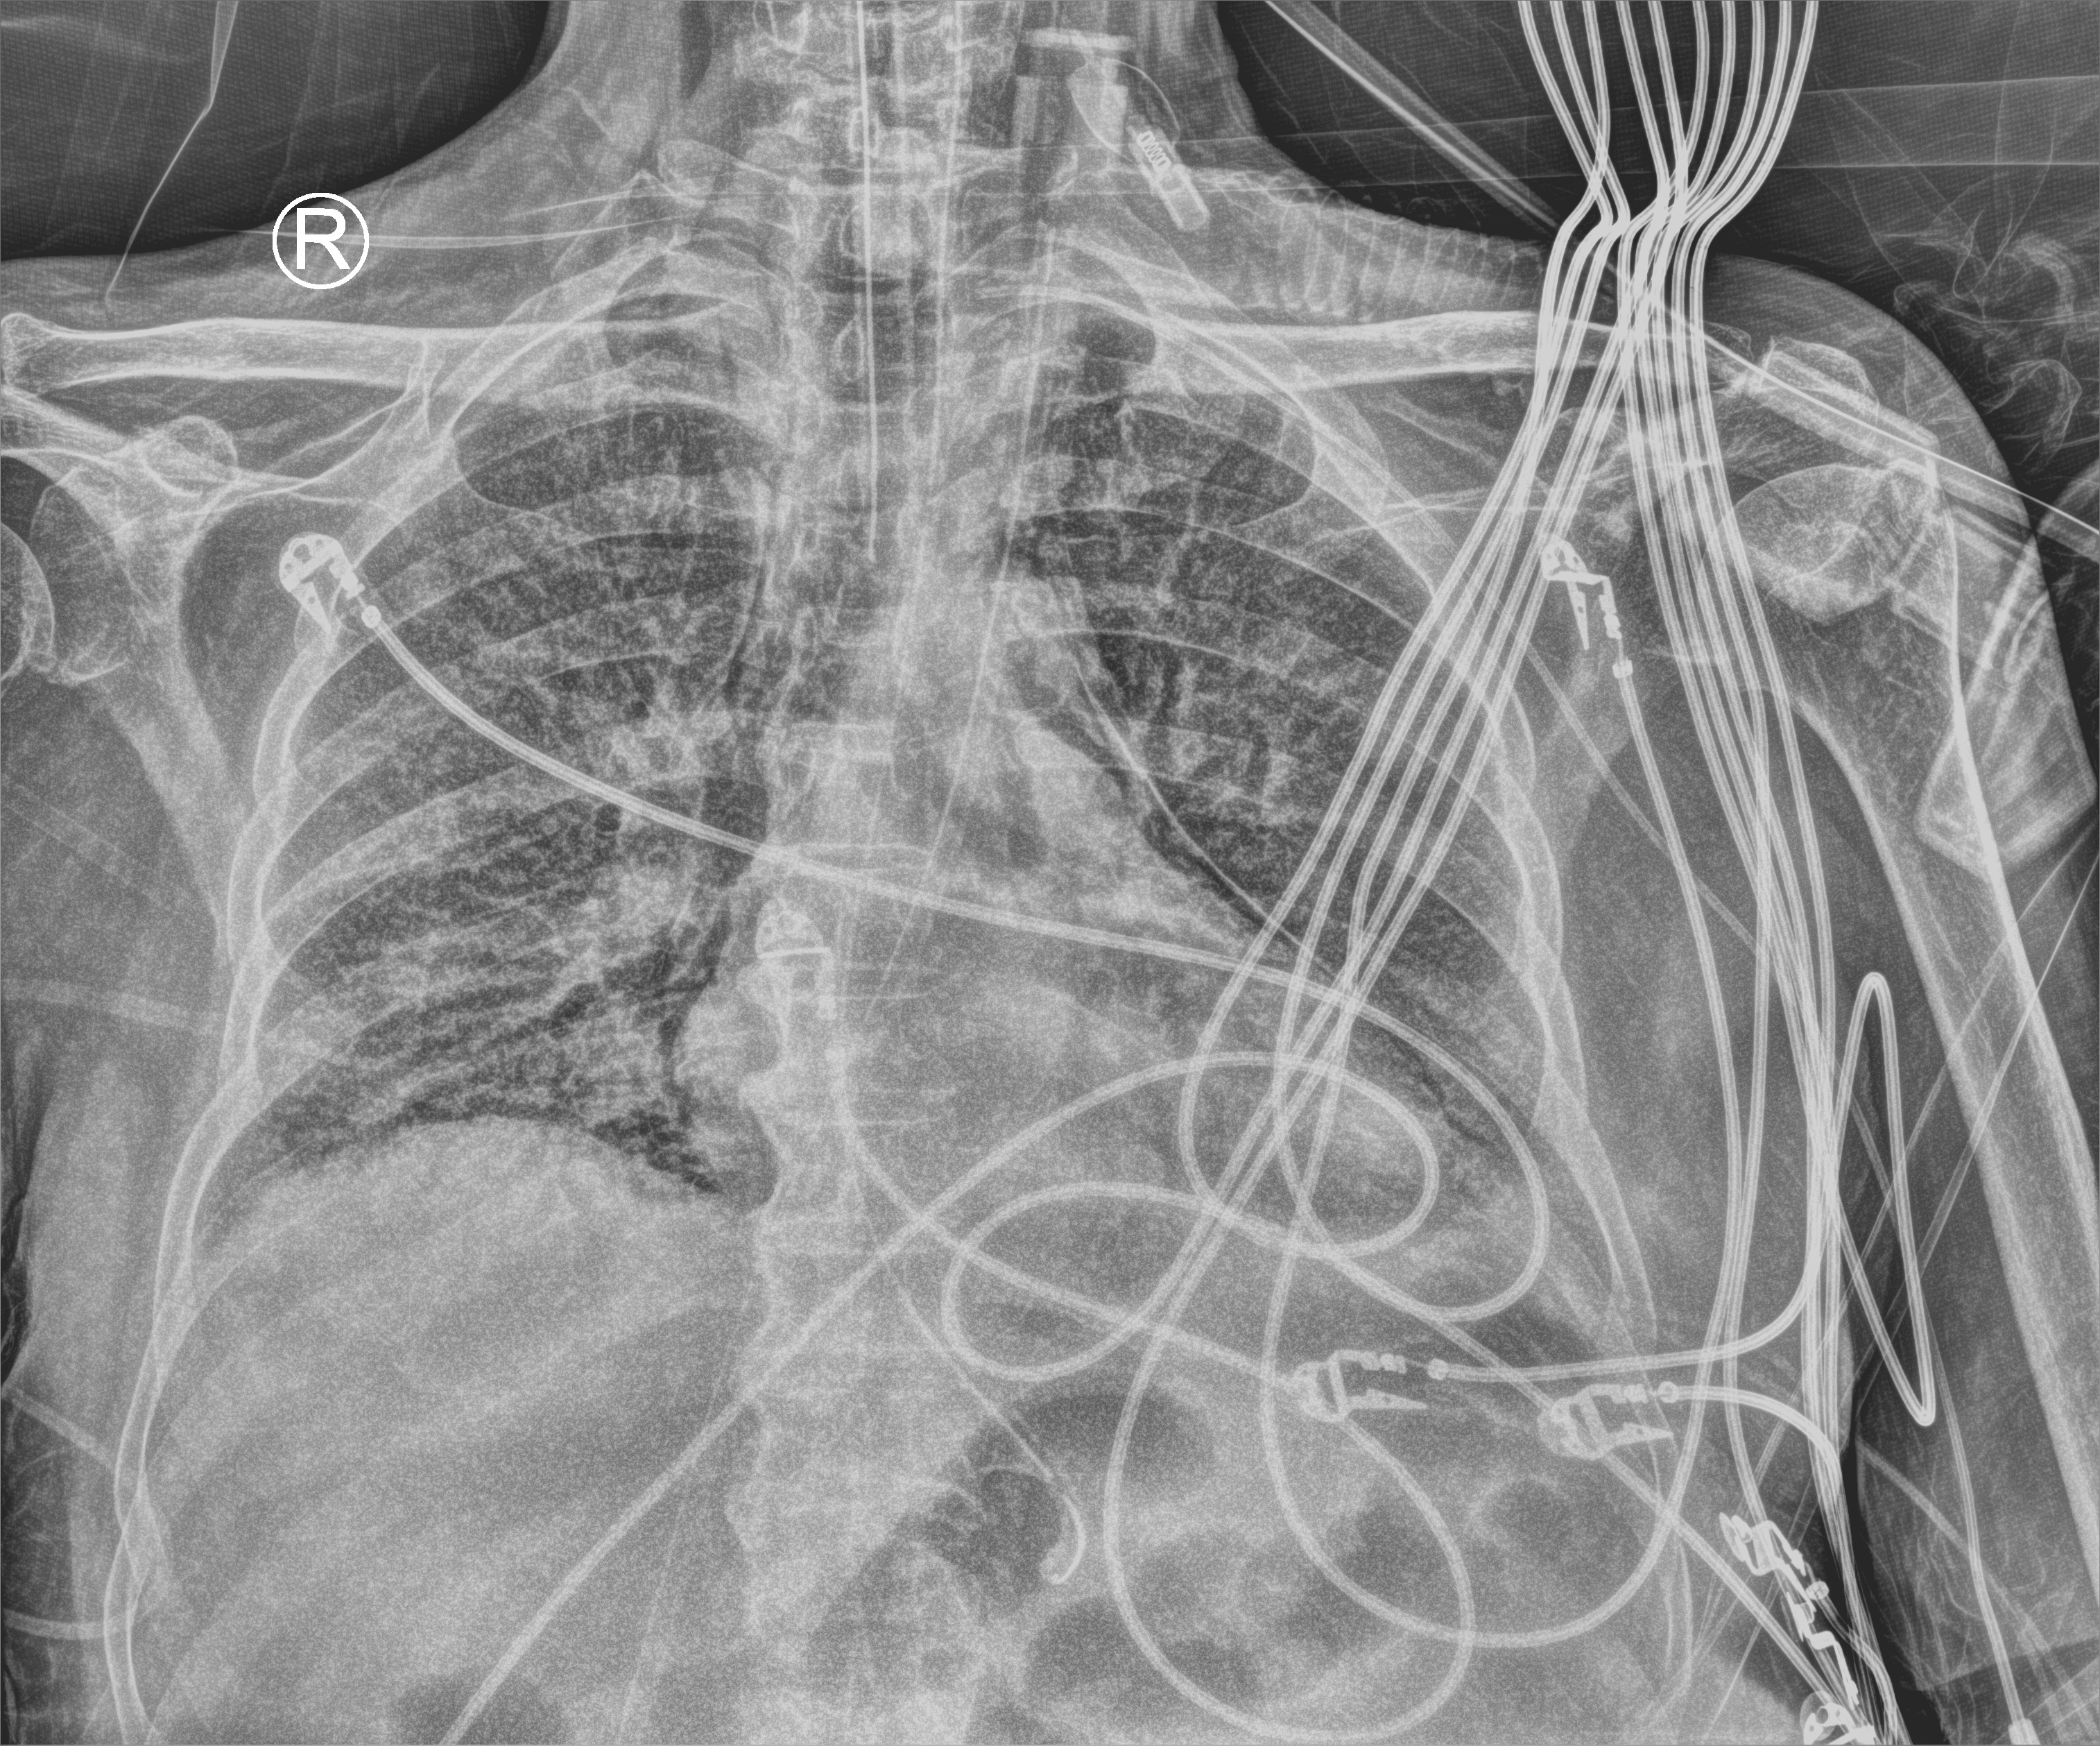
Chest X-ray (portable); anteroposterior (AP) projection. Male patient hospitalised with COVID-19, age 75–90 years.
From the hospital-stay record, not from the radiograph (when in the stay this image was taken is not recorded): mechanically ventilated during this hospital stay: yes.